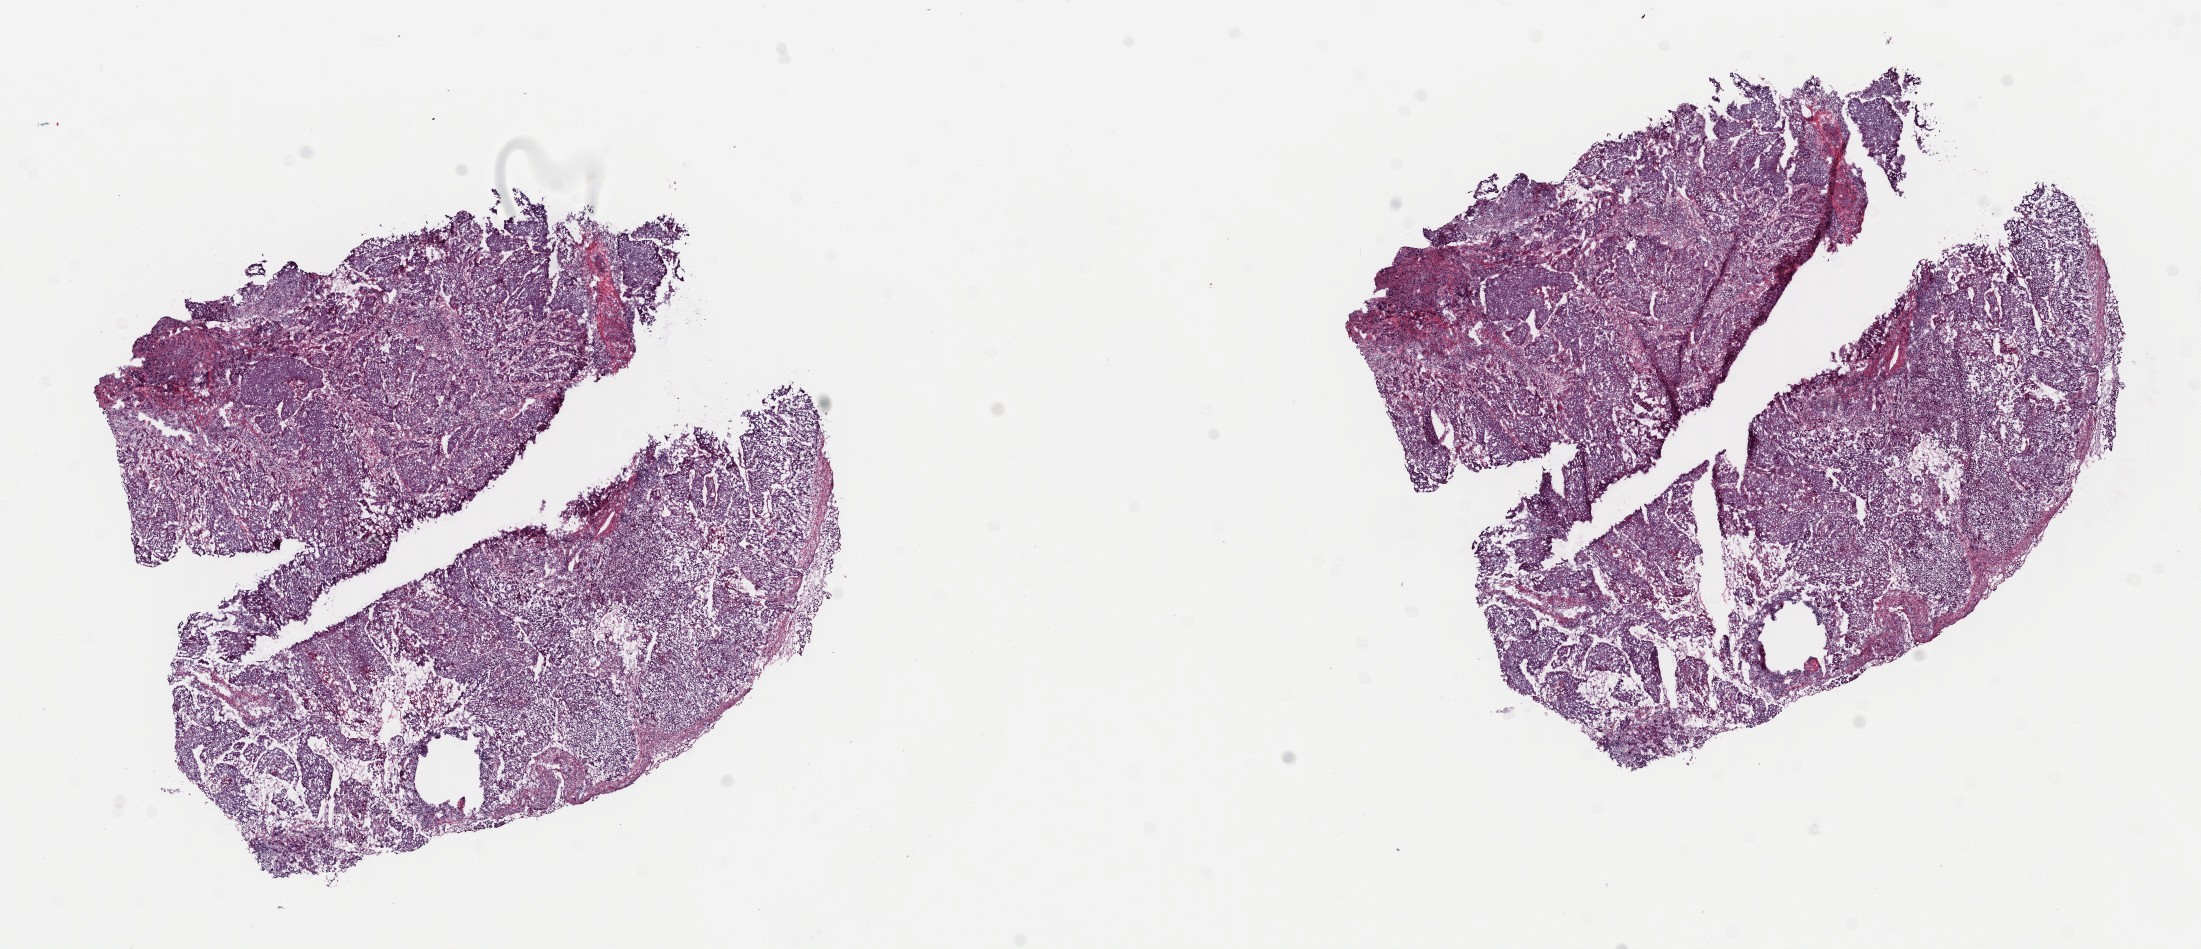
Digitized H&E tissue section (whole slide), low-resolution overview of the scanned area, about 17.4 x 7.5 mm (from a 40x scan); frozen section from the top of the tissue portion; sample: primary tumour, cervix. Patient: female, age at initial diagnosis 56 years. Histologic grade: G3 (poorly differentiated). Composition of this section per pathologist review: tumour cells 90%, tumour nuclei 90%, normal cells 0%, stromal cells 10%, necrosis 0%. Inflammatory infiltration, as recorded: lymphocyte infiltration 40%, monocyte infiltration 20%, neutrophil infiltration 20%.
FIGO stage: IIB. Pathologic diagnosis: Squamous cell carcinoma, NOS (cervix uteri).